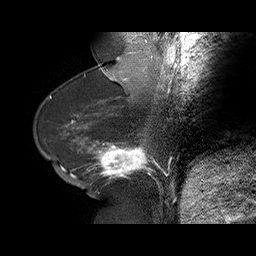
Breast MRI (dynamic contrast-enhanced), one sagittal slice. Slice 27 of 75 in the series (ordered by position). Dynamic contrast-enhanced series, time point 2 of 6 at this slice position (early post-contrast). 1.5 T. TE 4.5 ms, TR 32.4 ms. 3 mm slice thickness. 256 × 256 image matrix, field of view 180 × 180 mm. Female patient. Case-level facts recorded for this patient, not image findings: setting: breast cancer imaged before/during neoadjuvant chemotherapy; receptor status: HR-positive, HER2-negative.
Structures marked on this image (semi-automatic segmentation, software-assisted and operator-edited):
- analysis volume of interest (the breast-tissue region the enhancement analysis was run in; not a lesion): bounding box <58,134,166,191> (left, top, right, bottom; pixels)
- tumour enhancement mask (voxels above the 100 % enhancement threshold inside the analysis volume of interest): <61,137,165,178>